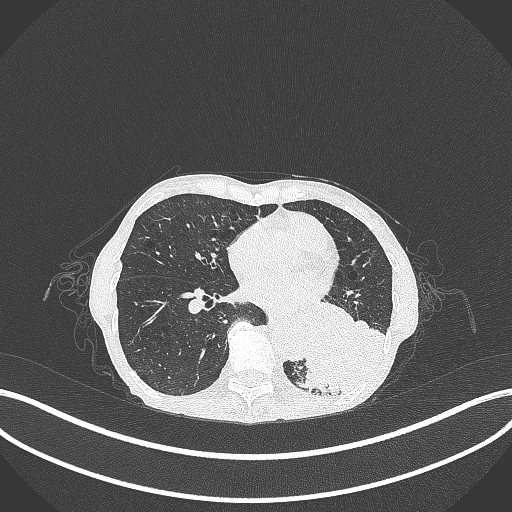
Chest CT, one axial slice; slice 107 of 347 in the series (ordered by position); reconstruction kernel B70f; lung window (W 1500 / L -600 HU); 1 mm slice thickness; 512 × 512 image matrix, field of view 400 × 400 mm. Patient: female, 70 years. Case-level facts recorded for this patient, not image findings: clinical TNM (as recorded): T3 N0 M0; histopathological grade: G3.
Outlined on this slice (bounding box drawn by a radiologist):
- lung tumour (recorded histology: small cell carcinoma): bounding box (x1, y1, x2, y2) in pixels: (290, 306, 392, 396)